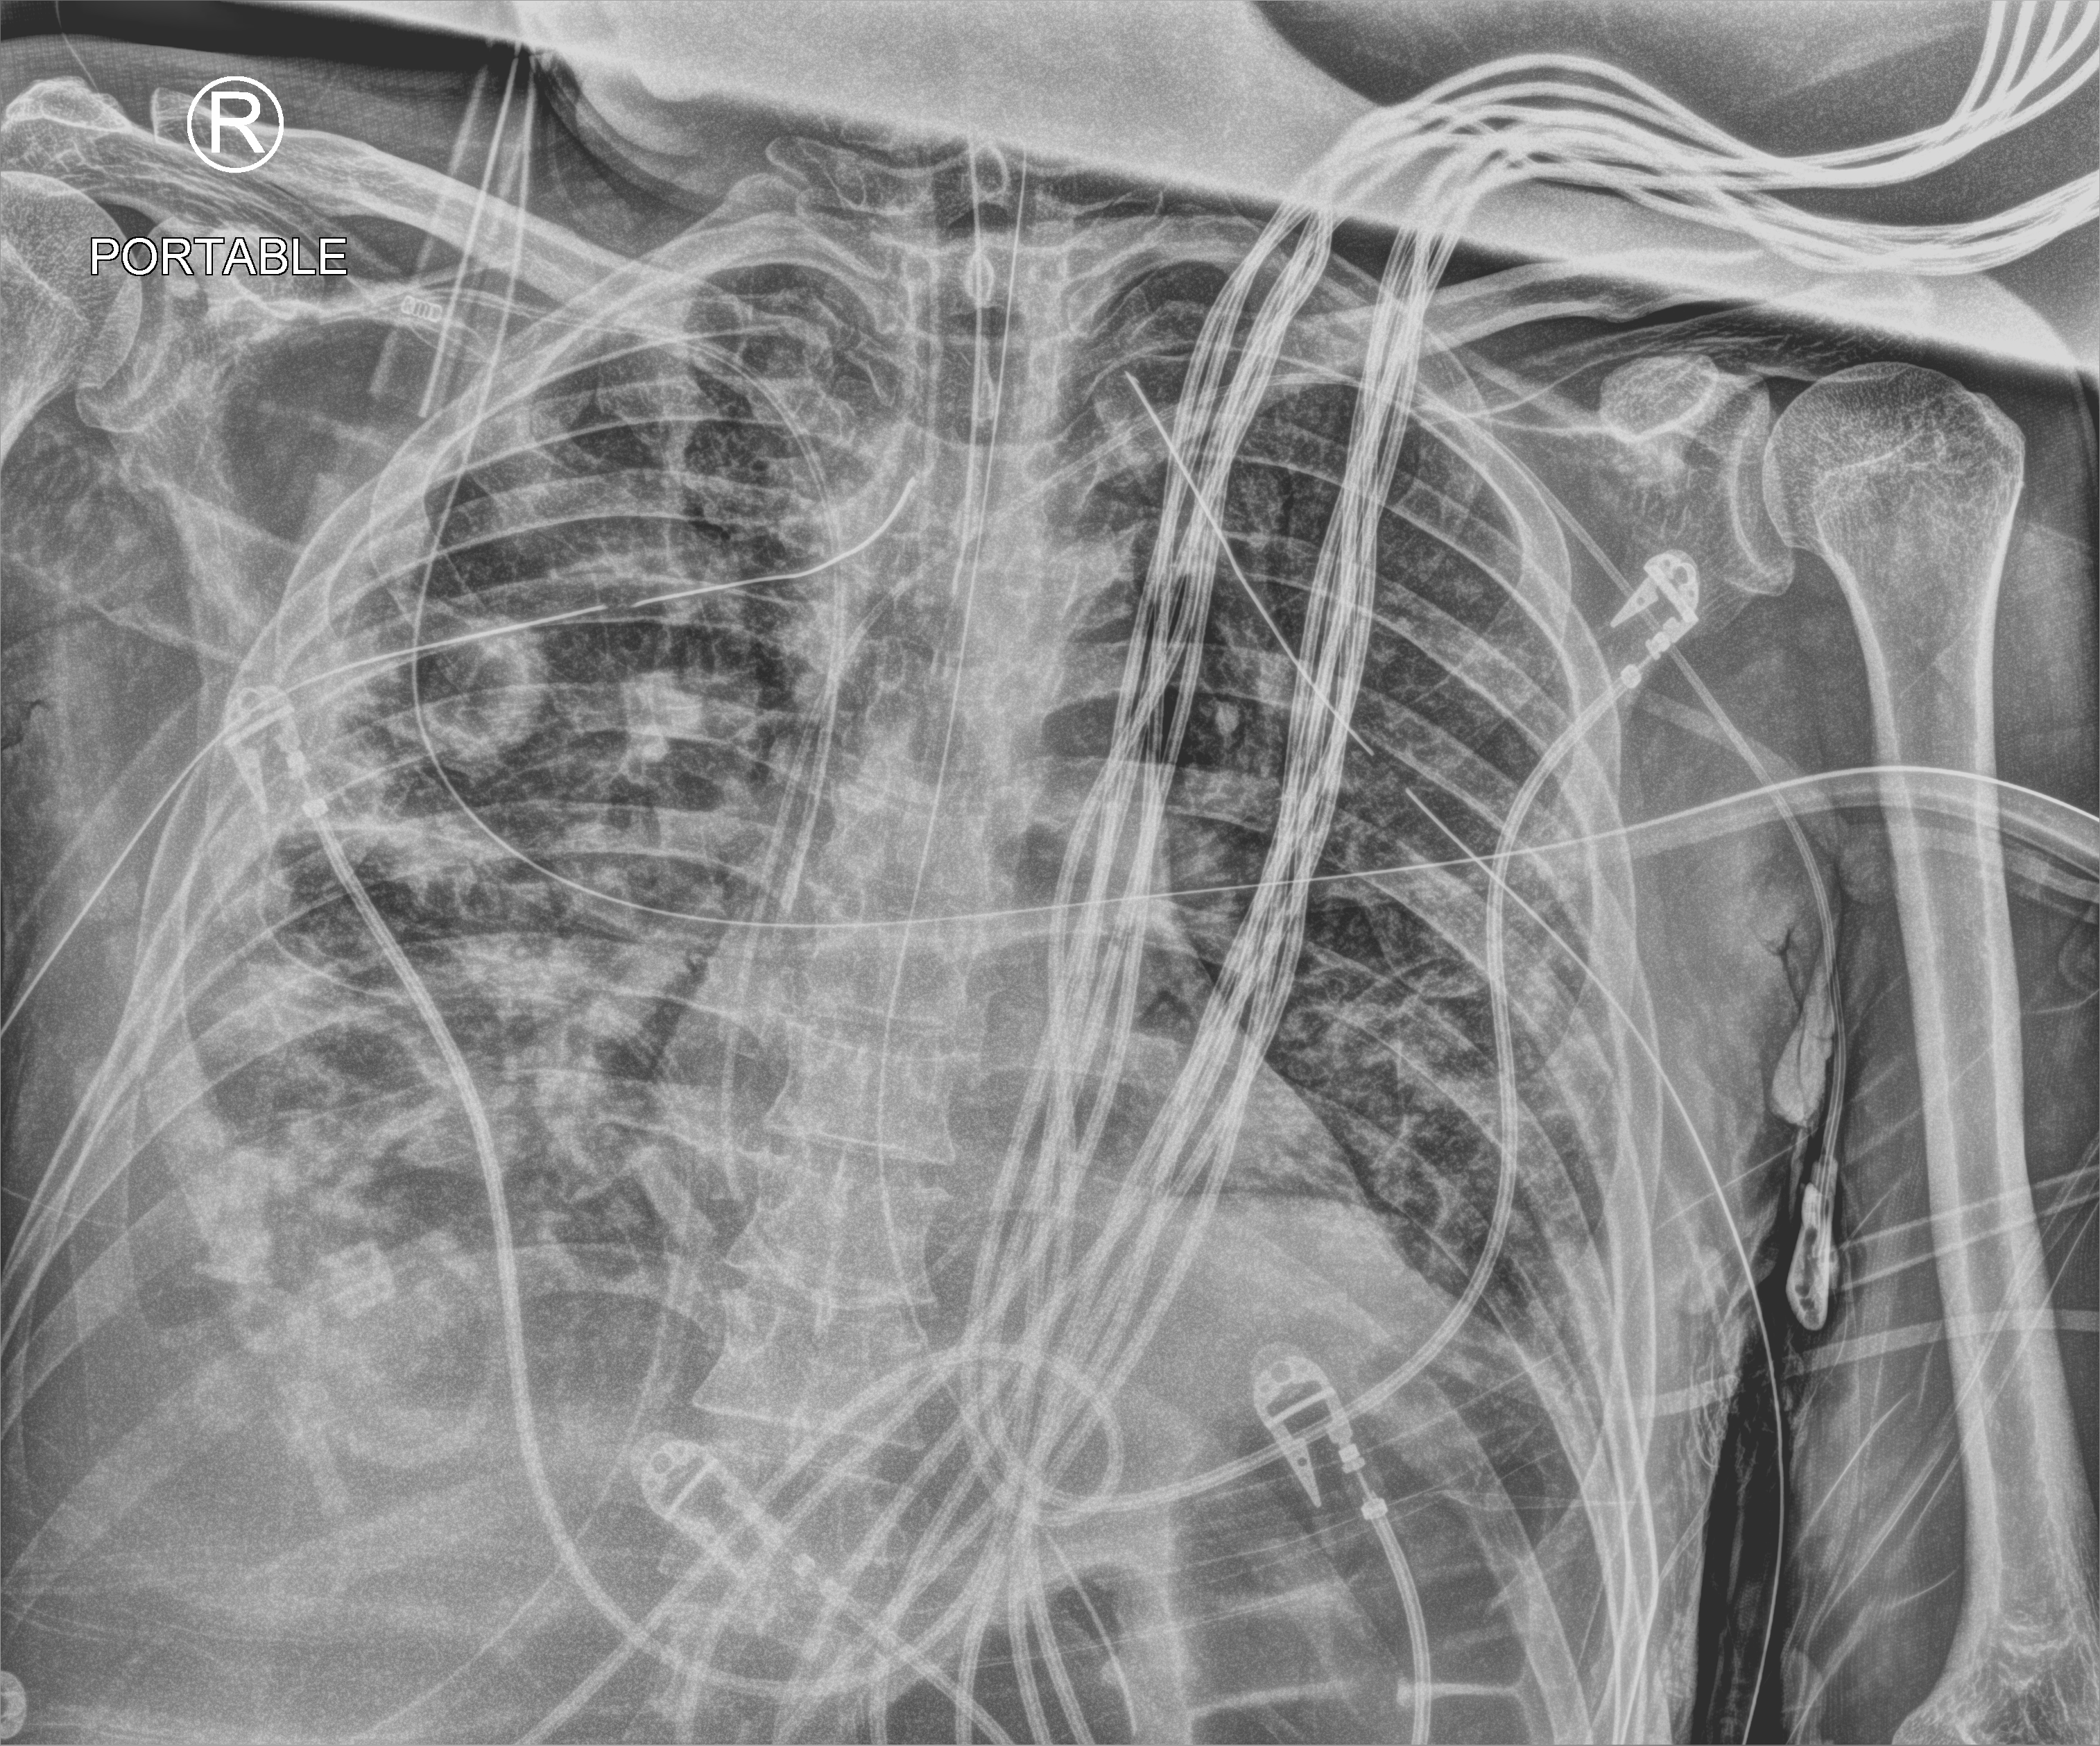
Portable chest radiograph, anteroposterior (AP) projection. Patient hospitalised with COVID-19; male, aged 18–59 years.
Admission-level facts for this patient (not findings on this image; timing relative to this image not recorded):
- admitted to intensive care during this hospital stay: yes